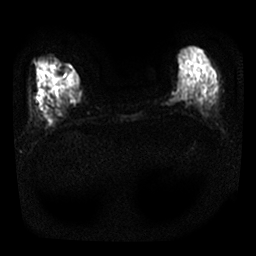
Breast MRI, one axial slice; slice 8 of 24 in the series (ordered by position); diffusion-weighted series; image 2 of 4 stored at this slice position (different b-values; order by instance number); 1.5 T; 4 mm slice thickness; 256 × 256 image matrix, field of view 300 × 300 mm. Female patient.
Outlined on this slice (manually delineated by an expert):
- tumour on diffusion-weighted imaging: bounding box [x1, y1, x2, y2] px = [165, 92, 182, 104]